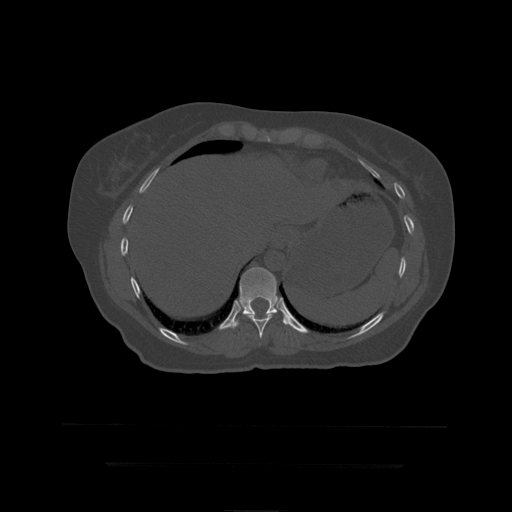
CT including the spine, one axial slice. Reconstruction kernel STANDARD. Bone window (W 1800 / L 400 HU). 1.25 mm slice thickness. 512 × 512 image matrix, field of view 450 × 450 mm. Patient age 41 years. From the clinical record (not read from this slice): primary cancer: breast.
Outlined on this slice (semi-automatically segmented with operator editing):
- T10 vertebra: box from (x=247, y=314) to (x=273, y=339) px
- T11 vertebra: (x=228, y=268)–(x=289, y=329)